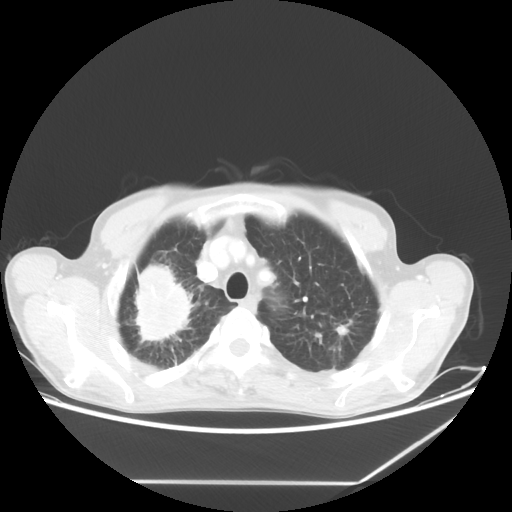
Chest CT, one axial slice. Slice 52 of 65 in the series (ordered by position). 80 kVp. Lung window (W 1500 / L -600 HU). 512 × 512 image matrix, field of view 397 × 397 mm. Patient: male, 68 years. Case-level facts recorded for this patient, not image findings: clinical TNM (as recorded): T3 N3 M0.
Annotated regions visible in this slice (rectangle marked by the reading radiologist):
- lung tumour (recorded histology: adenocarcinoma): bounding box <117,255,195,351> (left, top, right, bottom; pixels)